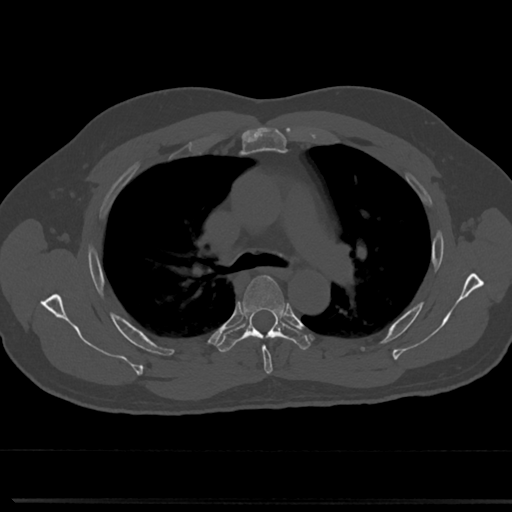
CT including the spine, one axial slice; slice 514 of 817 in the series (ordered by position); 120 kVp; bone window (W 1800 / L 400 HU); 0.5 mm slice thickness; 512 × 512 image matrix, field of view 355 × 355 mm. Patient: male, 61 years. From the clinical record (not read from this slice): primary cancer: prostate.
Outlined on this slice (semi-automatic segmentation, software-assisted and operator-edited):
- T4 vertebra: bounding box [x1, y1, x2, y2] px = [243, 275, 287, 370]
- T5 vertebra: [219, 299, 310, 351]